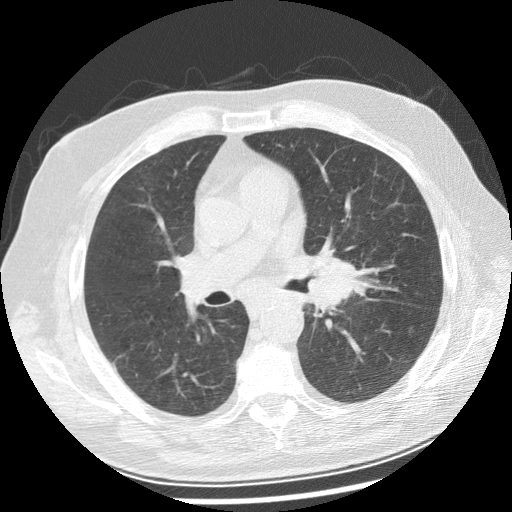
Chest CT (low-dose screening protocol), one axial image. Baseline annual screen. Lung window (W 1500 / L -600 HU). Standard (soft-tissue) reconstruction kernel (STANDARD). 120 kVp. Slice 109 of 250 in the series. 512 × 512 image matrix, field of view 360 × 360 mm. Male, age 70 years at enrolment. Current smoker at enrolment.
Expert-annotated lung lesion, box from (x=285, y=241) to (x=367, y=313) px. No non-calcified nodule or mass ≥4 mm was recorded by the screening reader at this exam. Participant outcome: lung cancer diagnosed 29 days after this screen — squamous cell carcinoma, keratinizing, NOS, left main stem bronchus, moderately differentiated (G2), stage IIIB (AJCC 6th edition), 40 mm at pathology.